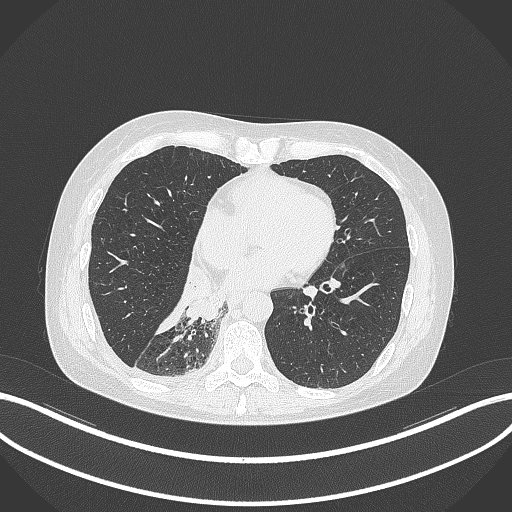
Chest CT, one axial slice. Slice 117 of 329 in the series (ordered by position). Reconstruction kernel B70f. 120 kVp. Lung window (W 1500 / L -600 HU). 1 mm slice thickness. 512 × 512 image matrix, field of view 400 × 400 mm. Patient: female, 63 years. Case-level facts recorded for this patient, not image findings: clinical TNM (as recorded): T1c N0 M0.
Structures marked on this image (bounding box drawn by a radiologist):
- lung tumour (recorded histology: adenocarcinoma): box from (x=182, y=265) to (x=223, y=323) px